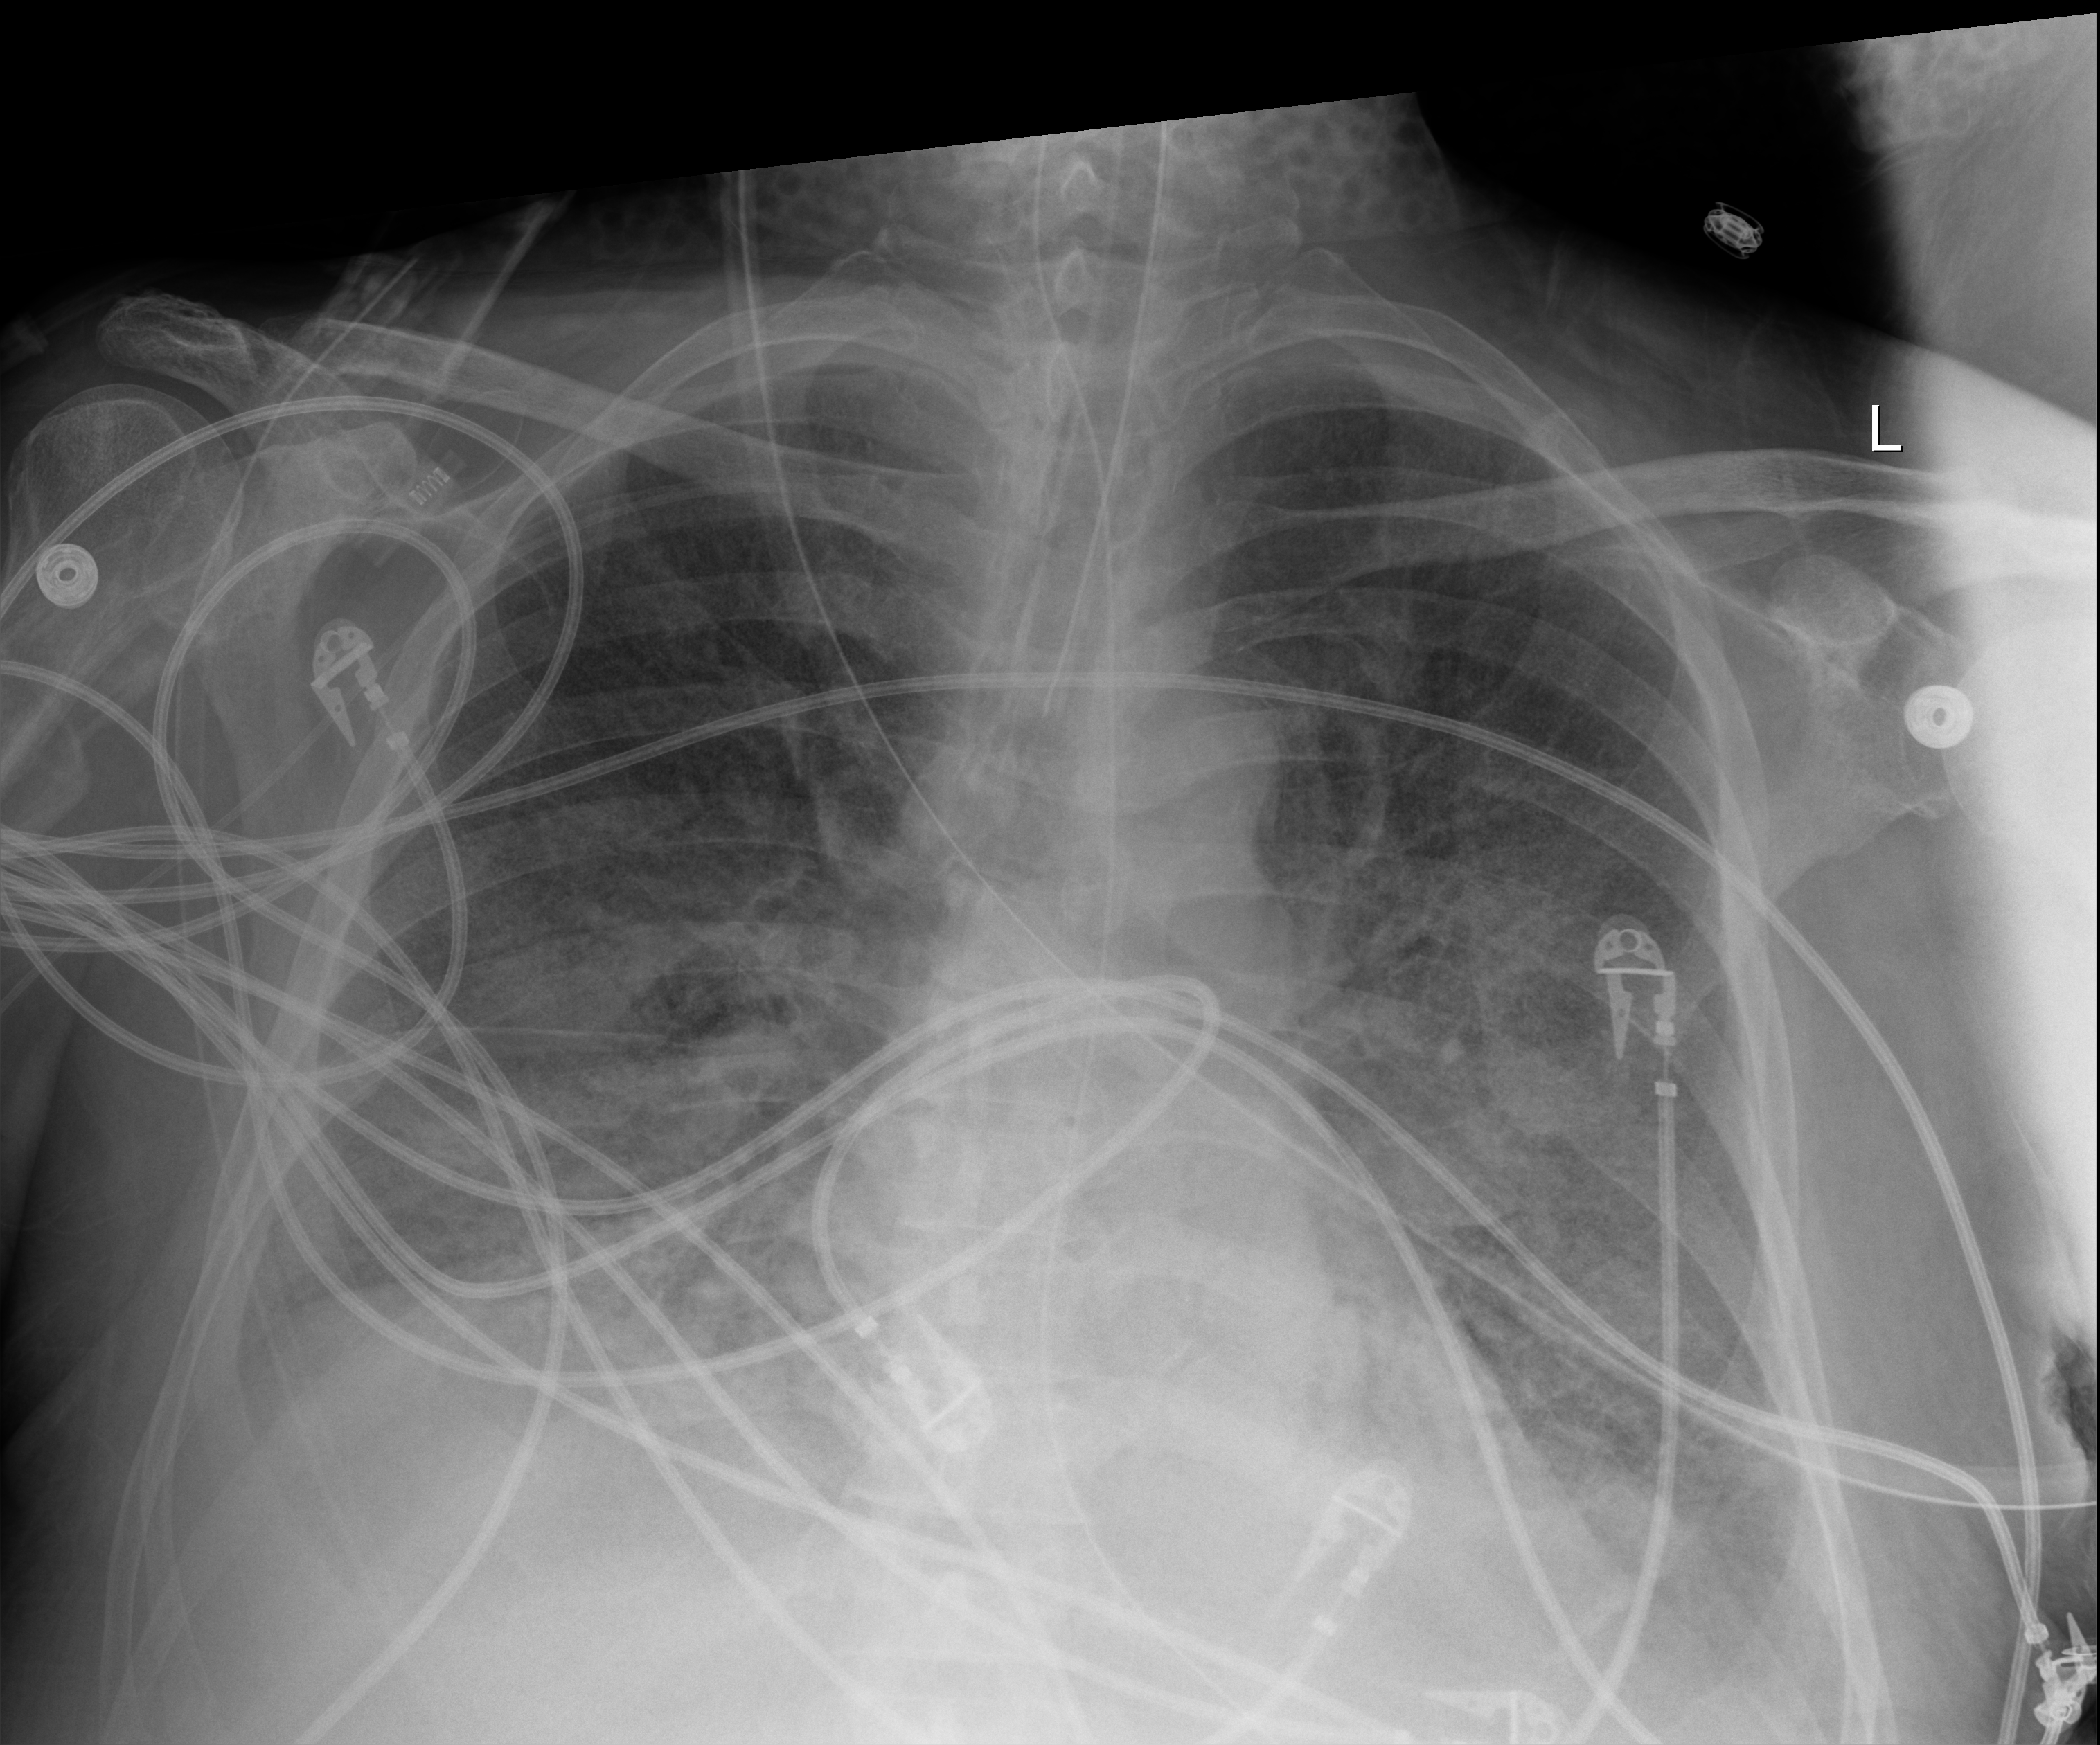
Portable chest radiograph, anteroposterior (AP) projection. Patient hospitalised with COVID-19; male, aged 60–74 years.
Admission-level facts for this patient (not findings on this image; timing relative to this image not recorded):
- admitted to intensive care during this hospital stay: yes